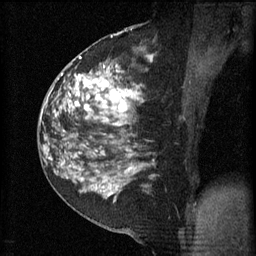
Breast MRI (dynamic contrast-enhanced), one sagittal slice. Position 26 of 60 along the scan axis. 3 images stored at this slice position (order not interpretable as contrast timing). 1.5 T. TE 4.2 ms, TR 11 ms. 256 × 256 image matrix, field of view 180 × 180 mm. Female patient, age 52 years.
Structures marked on this image (semi-automatically segmented with operator editing):
- analysis volume of interest (the breast-tissue region the enhancement analysis was run in; not a lesion): bounding box (x1, y1, x2, y2) in pixels: (81, 52, 155, 157)
- tumour enhancement mask (voxels above the 70 % enhancement threshold inside the analysis volume of interest): (81, 58, 141, 157)